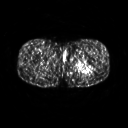
FDG PET of an extremity soft-tissue mass (from a PET/CT study), one axial slice; slice 245 of 267 in the series (ordered by position); 3.27 mm slice thickness; 128 × 128 image matrix. Patient: male, 27 years. From the clinical record (not read from this slice): histological type: extraskeletal osteosarcoma; grade: high; site of the primary tumour: left adductur.
Annotated regions visible in this slice (expert contour drawn on MRI and transferred to this co-registered scan by the dataset authors):
- gross tumour volume (mass): bounding box [x1, y1, x2, y2] px = [72, 59, 95, 75]